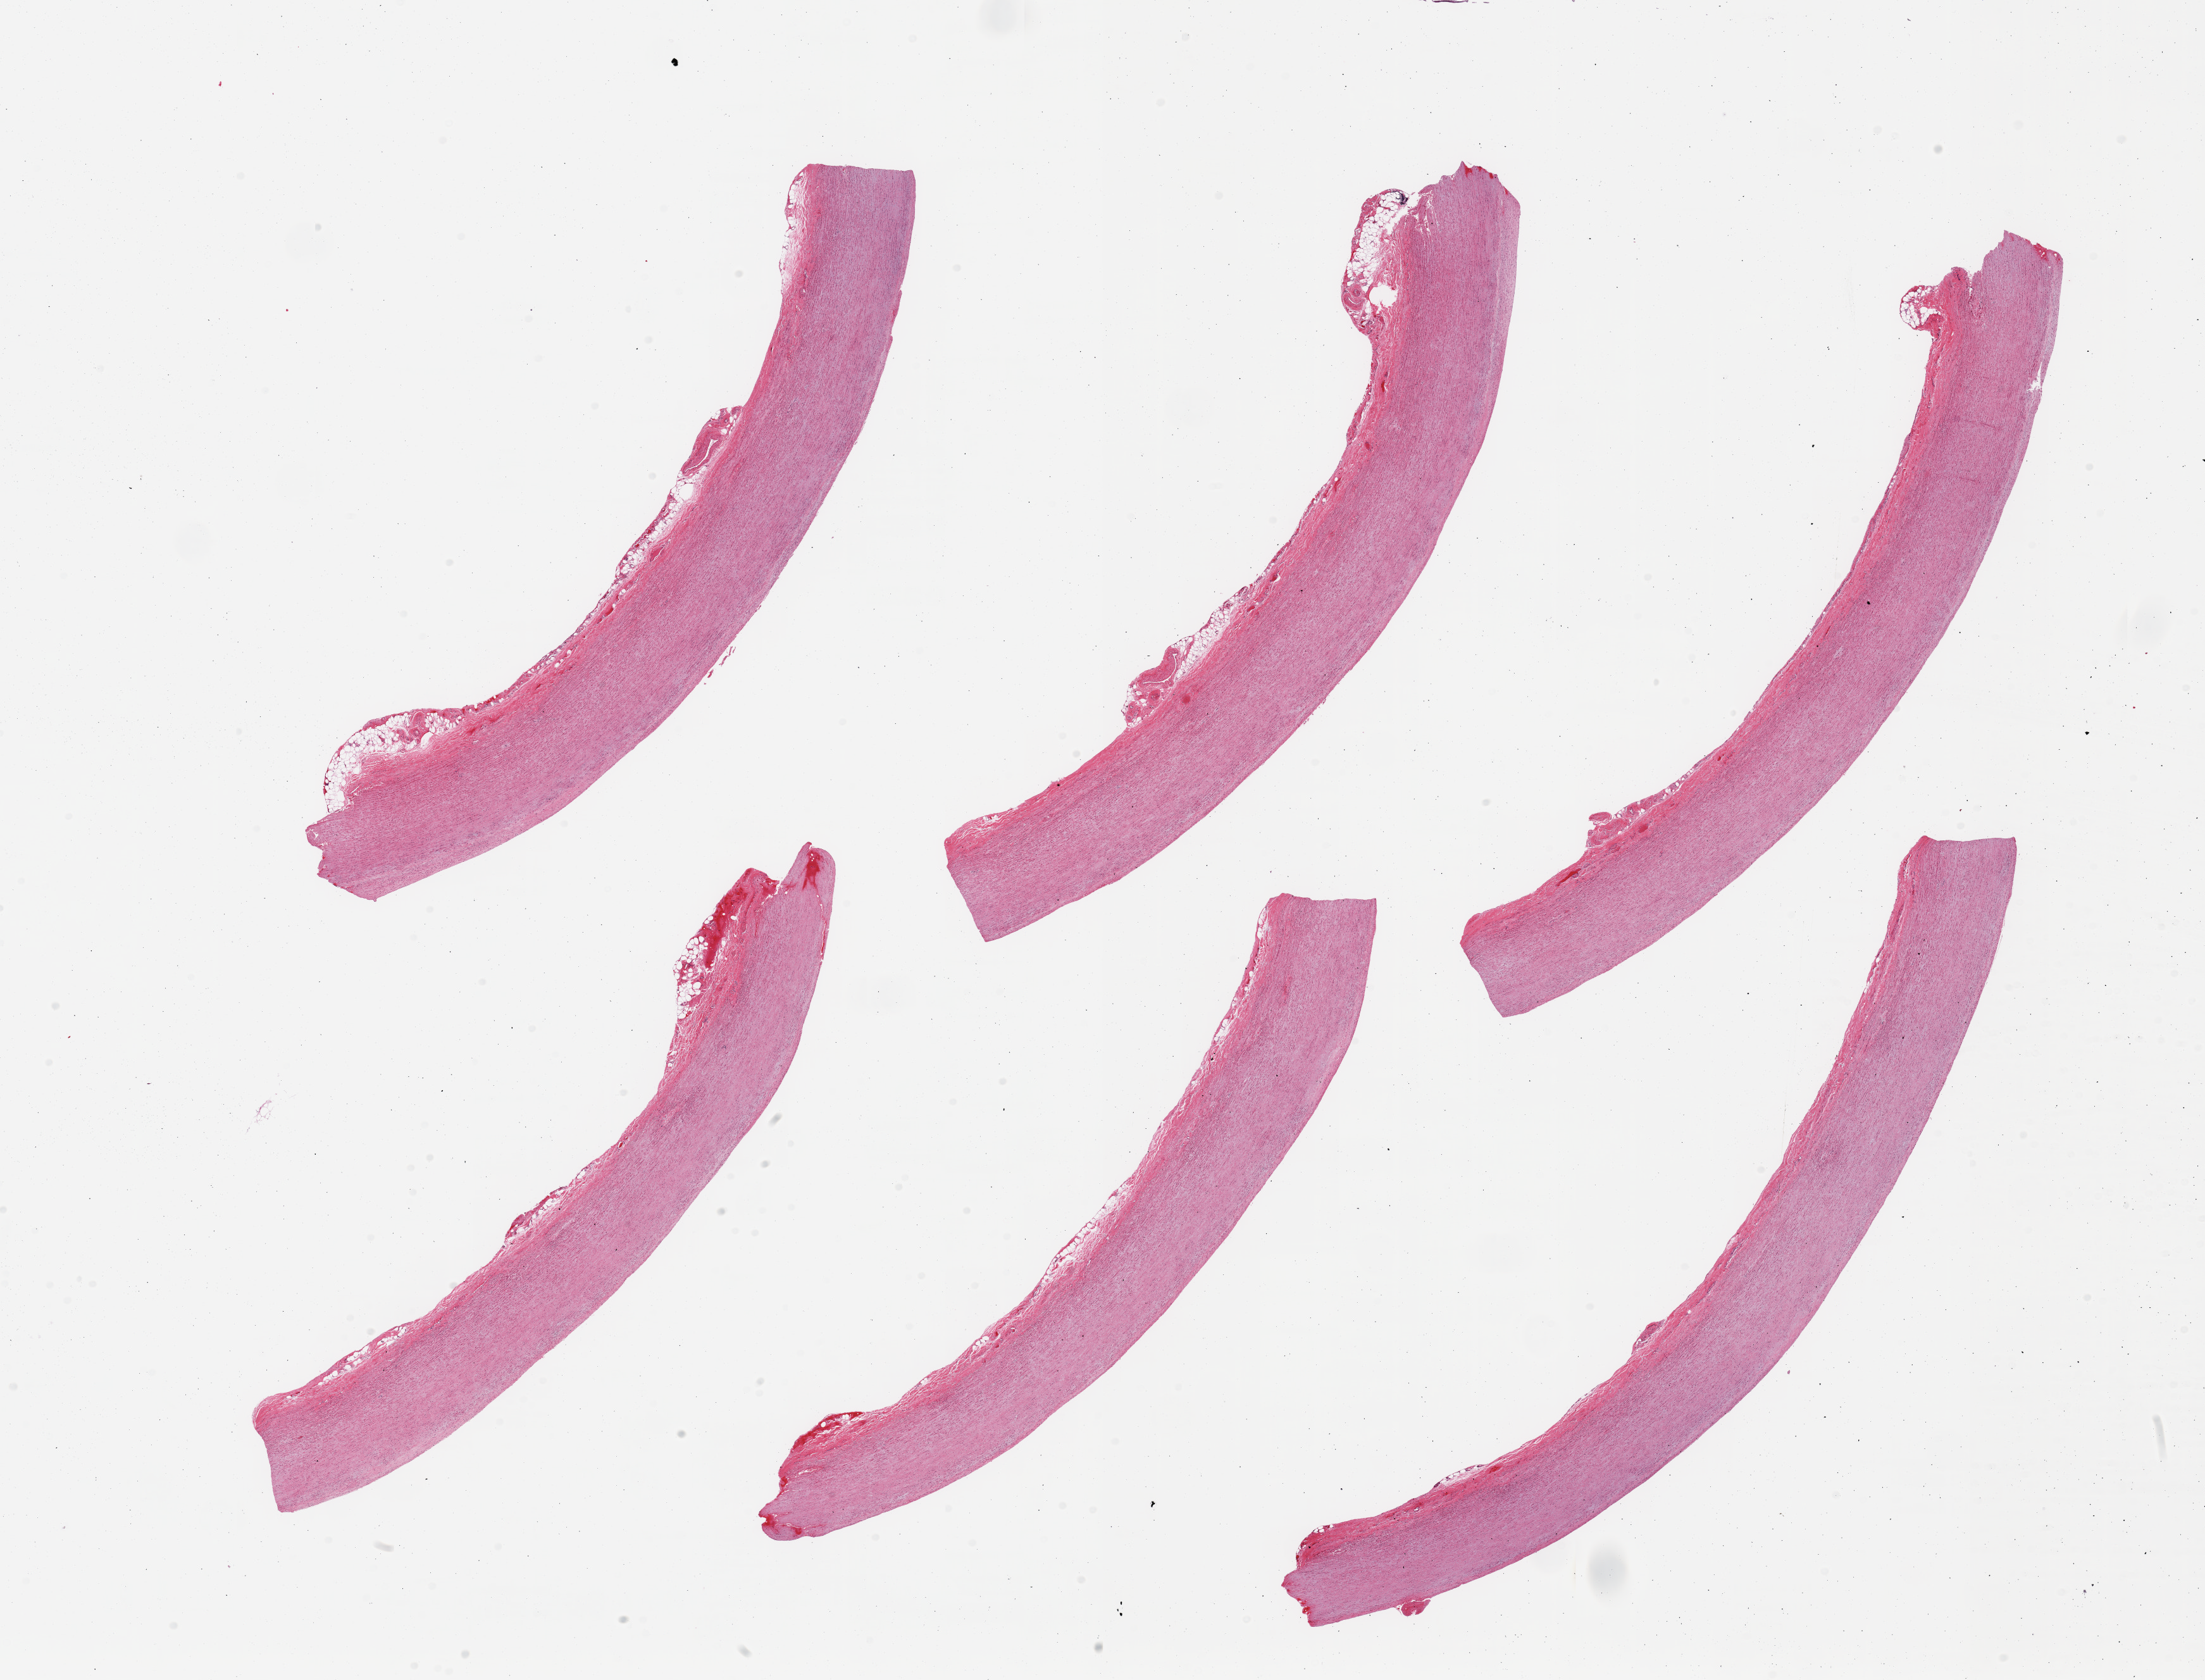
Haematoxylin and eosin whole-slide image — whole scanned area (about 27.6 x 21.0 mm, from a 20x scan) shown as a low-resolution overview; PAXgene-fixed paraffin-embedded (PFPE) section; target tissue: aorta; donor tissue sample.
Reviewer comment on this tissue sample: 6 pieces, minimal atherosis.